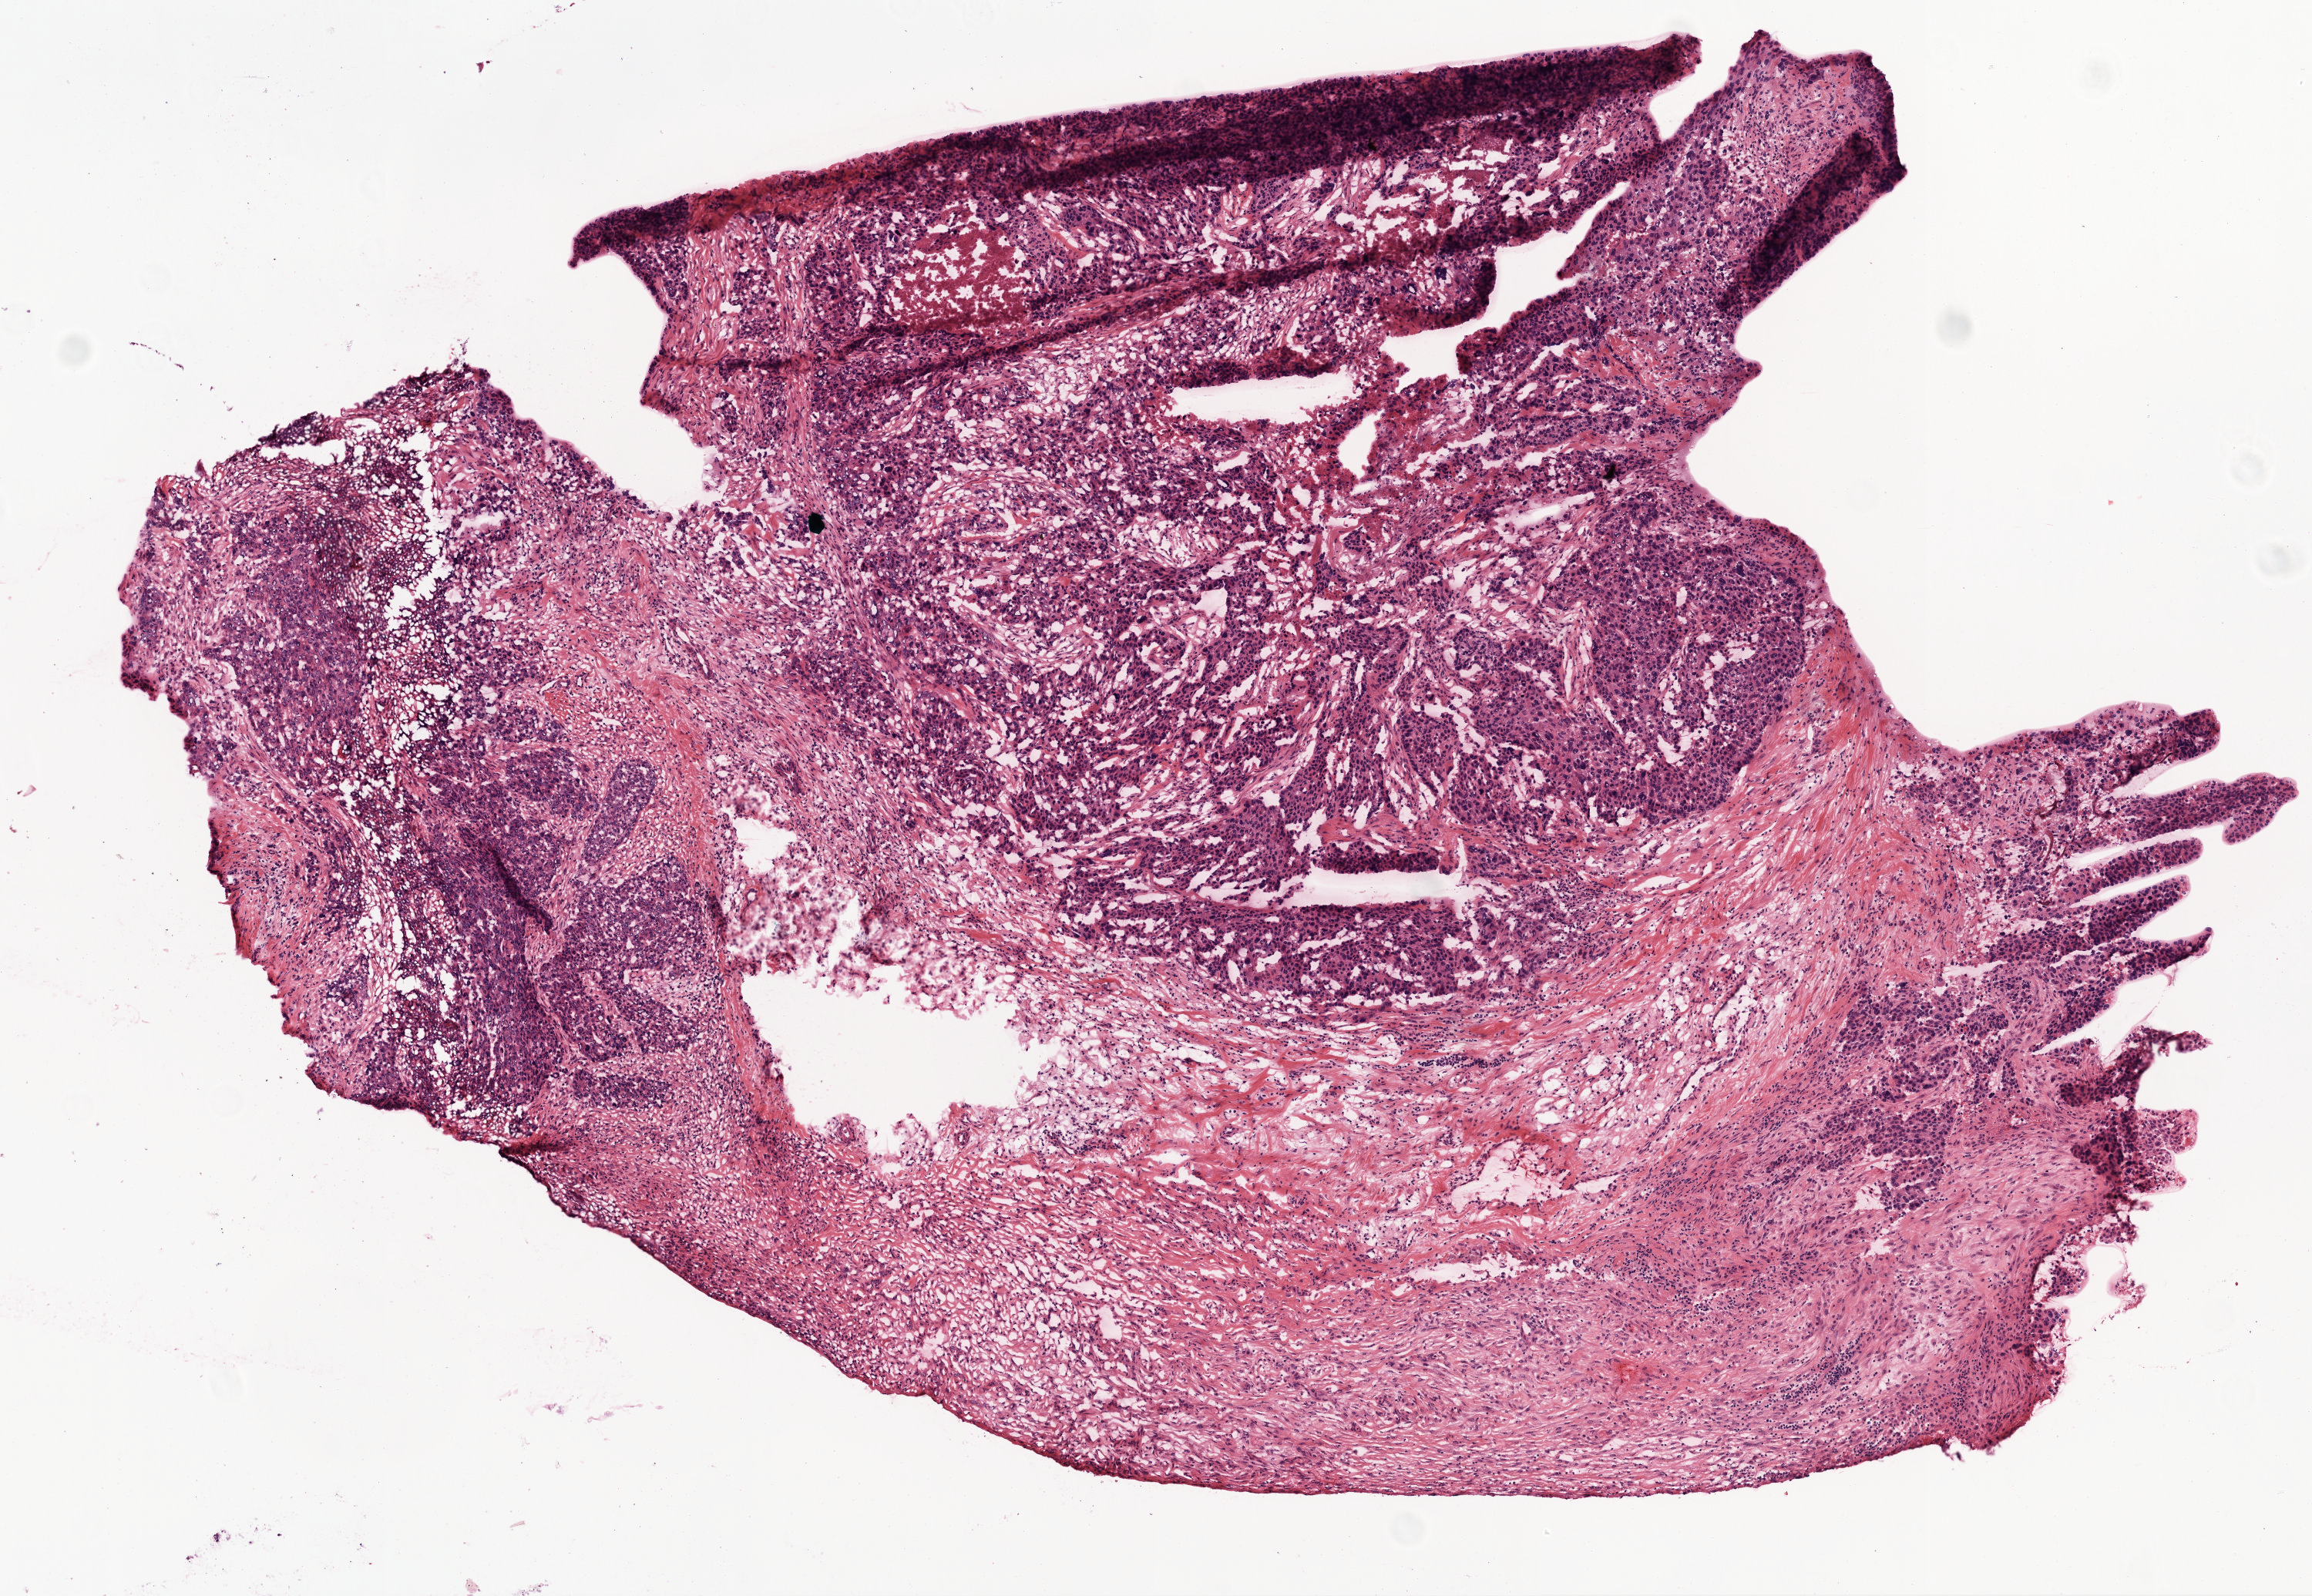
H&E whole-slide image — shown as a low-resolution overview of the whole scanned area (about 6.0 x 4.2 mm). Frozen section from the top of the tissue portion. Sample: primary tumour, ovary. Female patient; age at initial diagnosis 56 years. Slide review estimates, as recorded: tumour cells 60%, tumour nuclei 80%.
Histologic diagnosis: Serous cystadenocarcinoma, NOS.